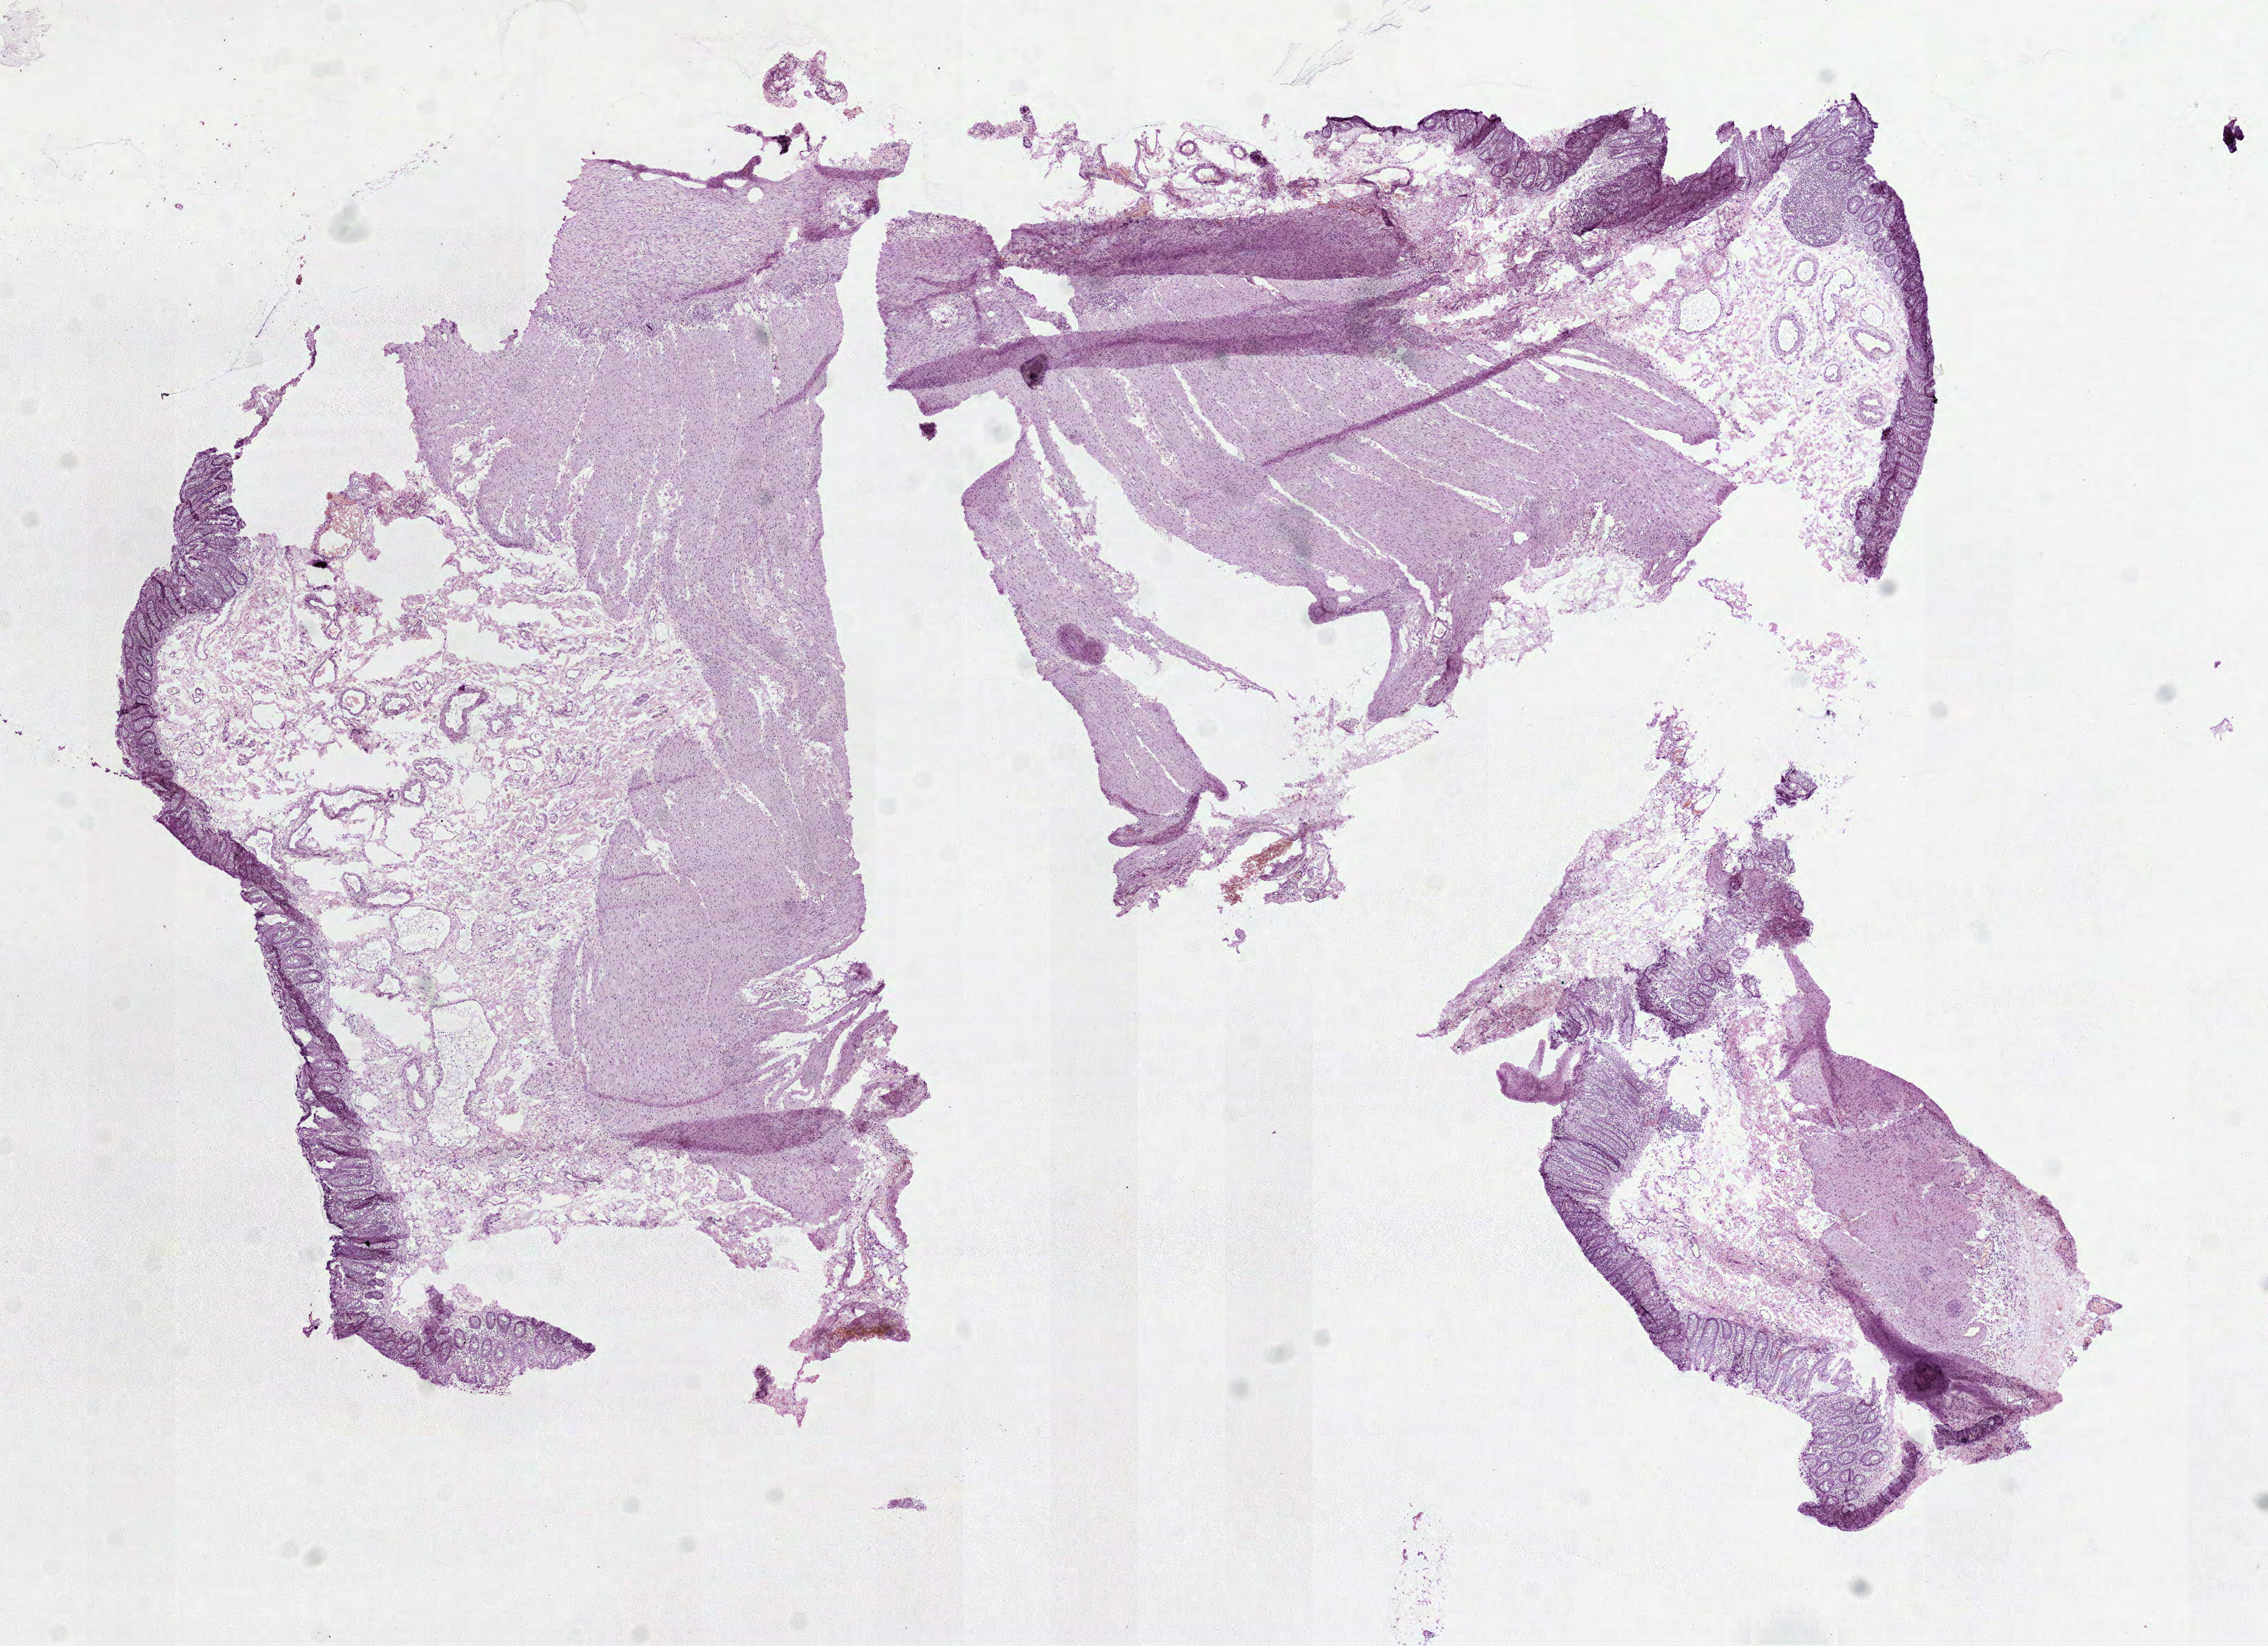
Whole-slide histology image, H&E-stained, whole scanned area (about 13.1 x 9.5 mm) shown as a low-resolution overview. Frozen section from the top of the tissue portion. Solid tissue normal (non-tumour tissue) sample from the colon. Patient sex: male.
• this section: solid tissue normal (non-tumour) sample from the same patient
• patient diagnosis: Adenocarcinoma, NOS (cecum)